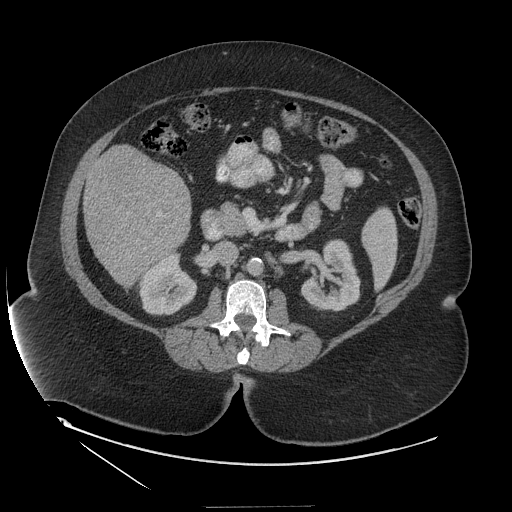
Contrast-enhanced abdominal CT (liver protocol), one axial slice. Reconstruction kernel STANDARD. Soft-tissue window (W 400 / L 40 HU). 512 × 512 image matrix, field of view 480 × 480 mm. From the clinical record (not read from this slice): diagnosis: hepatocellular carcinoma (patient treated with transarterial chemoembolisation; whether this scan precedes or follows treatment is not stated here); TNM stage (as recorded): Stage-II; Child-Pugh class: A; tumour differentiation: well differentiated; tumour nodularity: multinodular.
Structures marked on this image (semi-automatic segmentation, software-assisted and operator-edited):
- liver parenchyma outside the tumour (the mass and vessels are separate outlines, so this box may not span the whole liver): bounding box (x1, y1, x2, y2) in pixels: (84, 144, 190, 286)